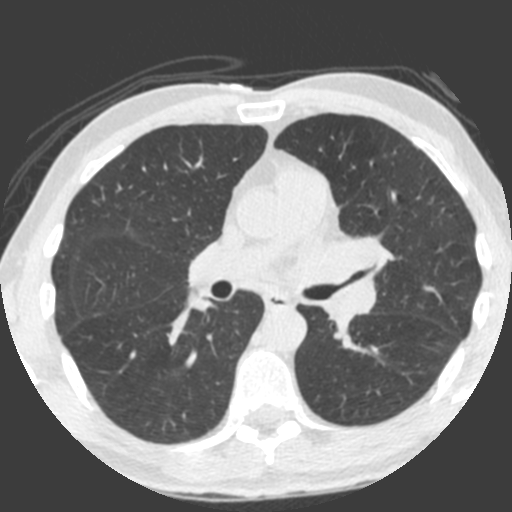
Low-dose screening chest CT, axial slice; third annual screen; lung window (W 1500 / L -600 HU); 2 mm slice thickness; slice 127 of 212 in the series. Male participant, aged 55 years at enrolment. Current smoker at enrolment.
Lesion marked by an expert reader, bounding box (x1, y1, x2, y2) in pixels: (308, 210, 402, 326). Reader record for this screening exam (exam-level; its link to the box is not recorded): non-calcified nodule or mass ≥4 mm, left upper lobe, 49 × 29 mm, spiculated (stellate) margins, soft tissue attenuation, pre-existing on the prior screen: yes; interval growth: yes. Official screen result: positive, other. Participant outcome: lung cancer diagnosed 0 days after this screen — small cell carcinoma, NOS, left upper lobe, undifferentiated (G4), stage IV (AJCC 6th edition), 60 mm at pathology.